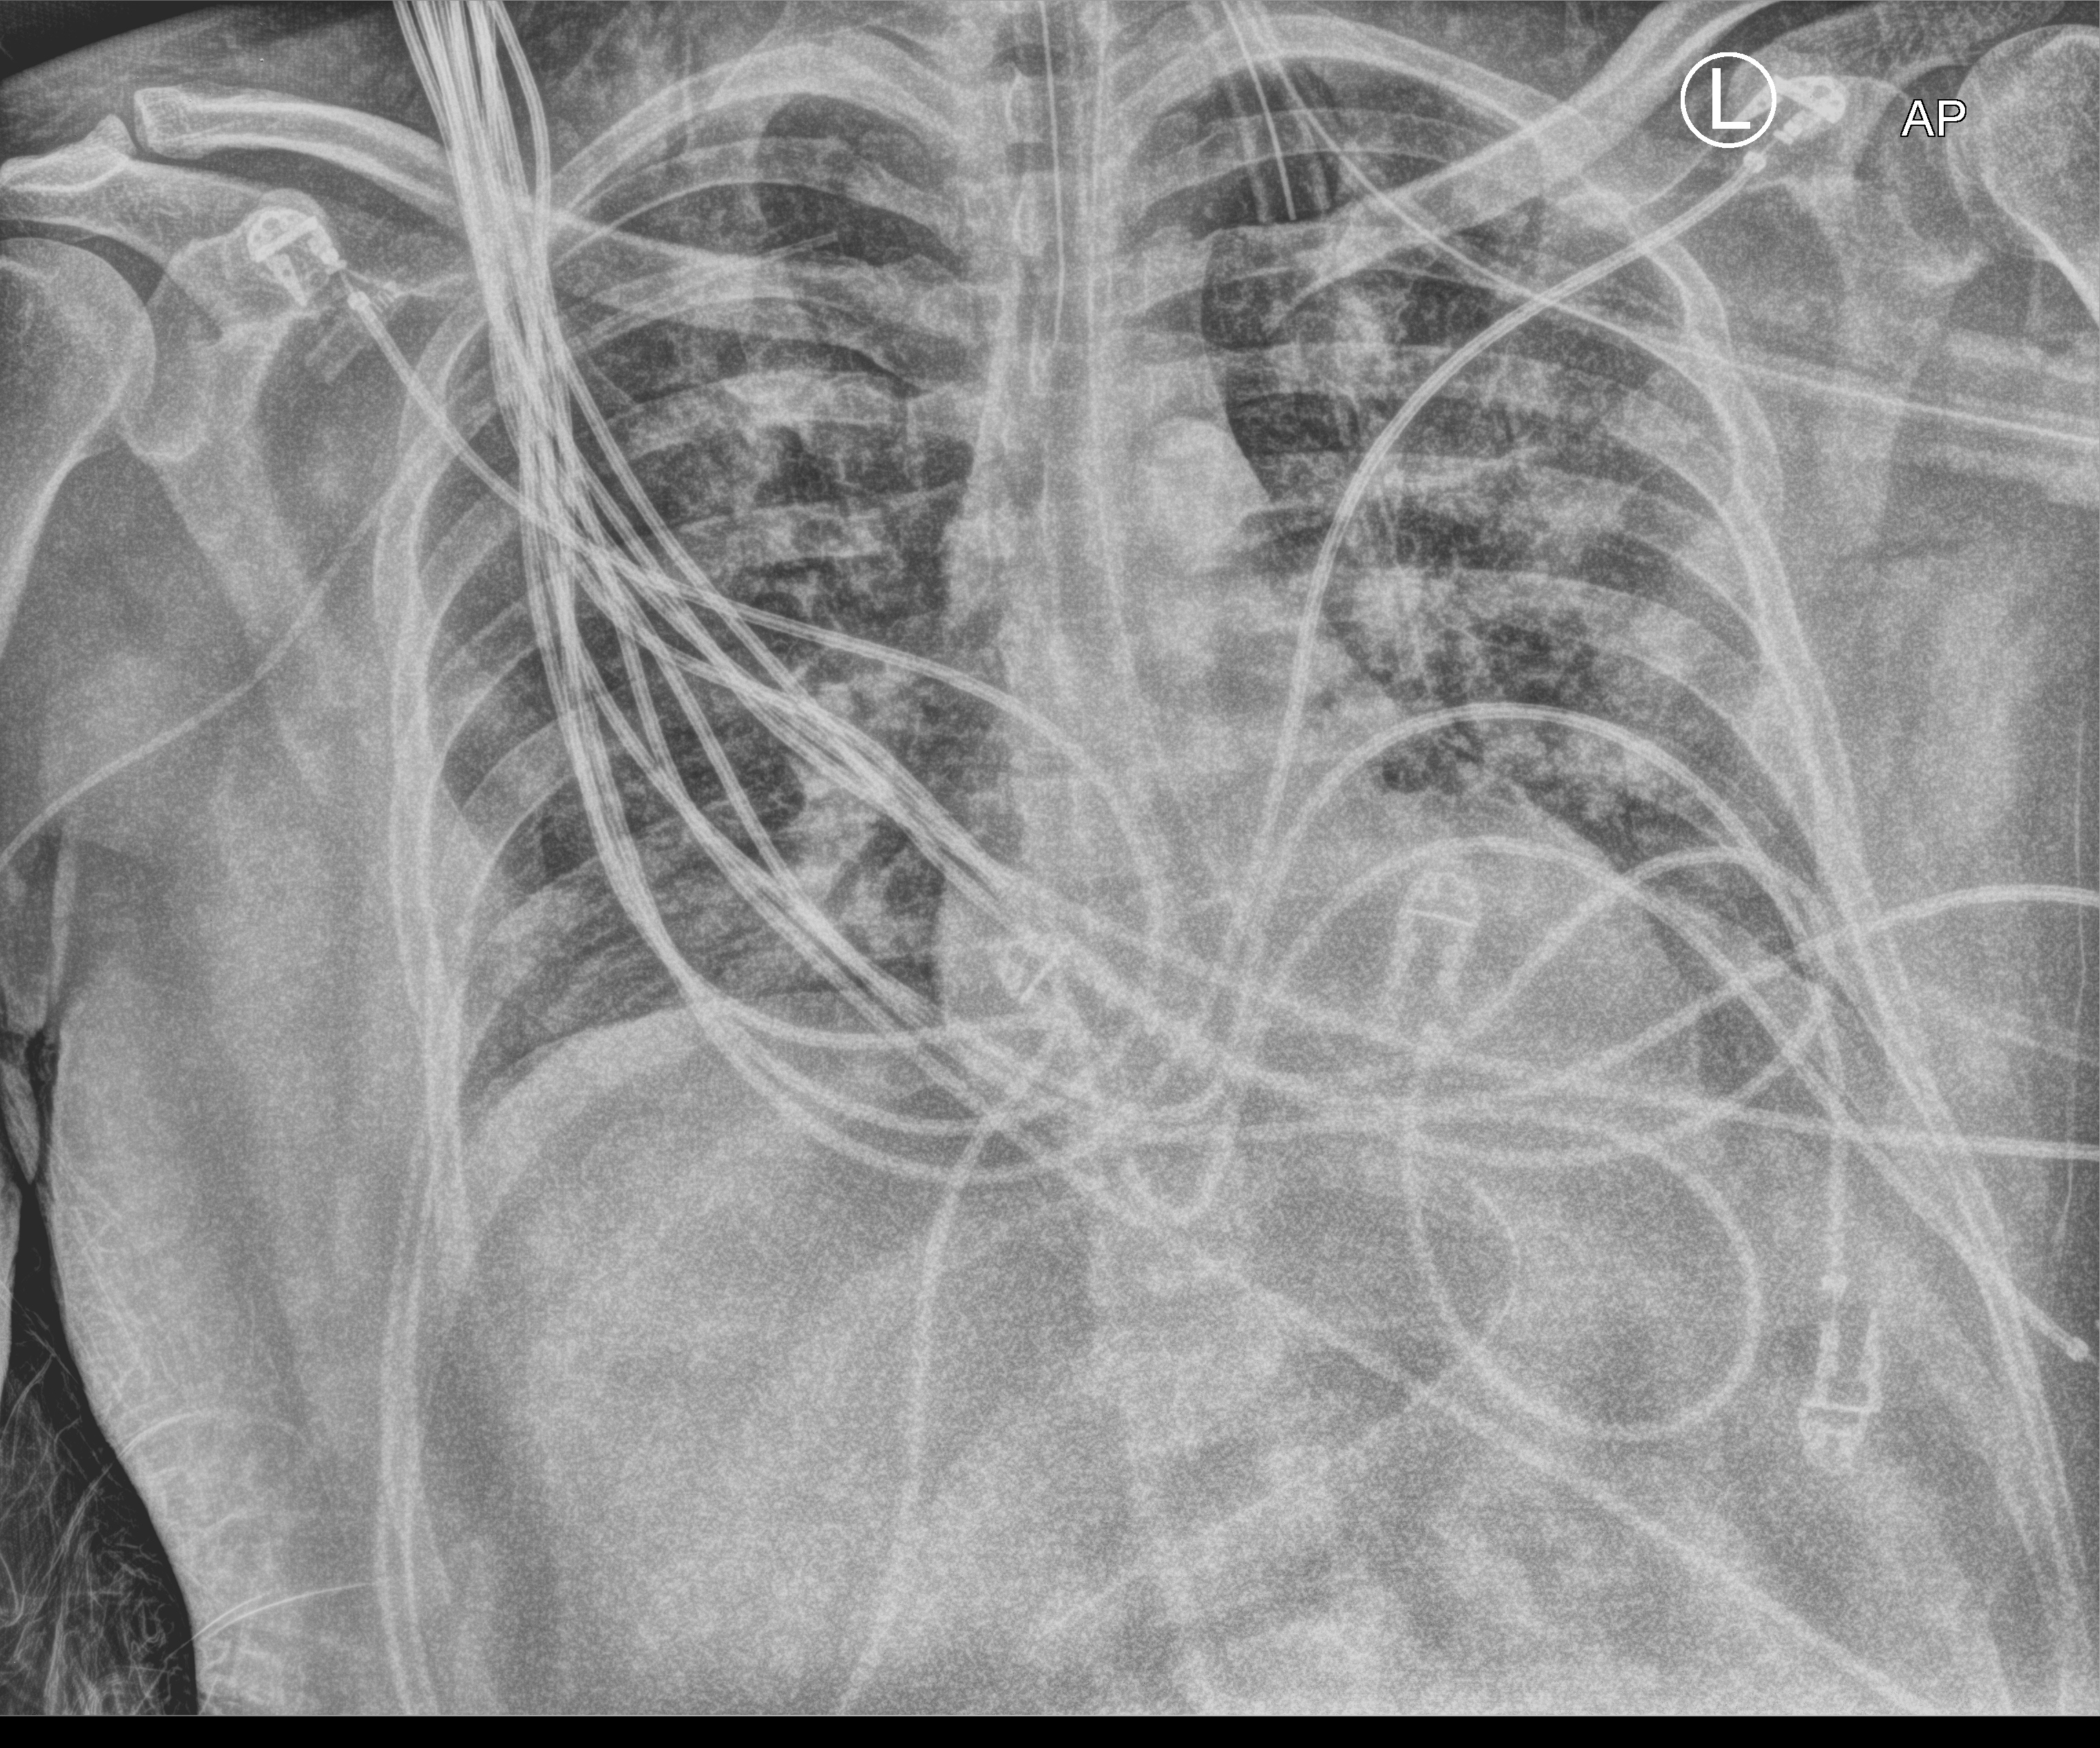
Bedside chest radiograph (computed radiography); anteroposterior (AP) projection. Male patient hospitalised with COVID-19, age 18–59 years.
From the hospital-stay record, not from the radiograph (when in the stay this image was taken is not recorded): other chronic lung disease (admission record): no; mechanically ventilated during this hospital stay: yes.